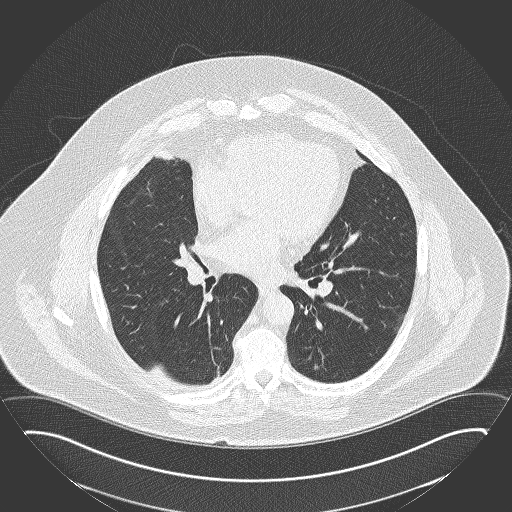
Low-dose screening chest CT, axial slice; second annual screen; lung window (W 1500 / L -600 HU); slice 95 of 180 in the series. Male participant, aged 63 years at enrolment. Former smoker at enrolment.
Expert-annotated lung lesion, bounding box [x1, y1, x2, y2] px = [294, 349, 341, 388]. Reader record for this screening exam (exam-level; its link to the box is not recorded): non-calcified nodule or mass ≥4 mm, left lower lobe, 12 × 12 mm, poorly defined margins, ground glass attenuation, pre-existing on the prior screen: no. Participant outcome: lung cancer diagnosed 550 days after this screen — squamous cell carcinoma, NOS, left lower lobe, moderately differentiated (G2), stage IA (AJCC 6th edition), 15 mm at pathology.